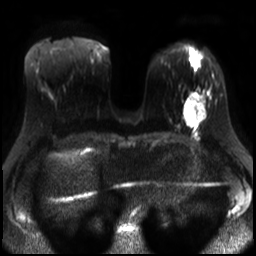
Breast MRI, one axial slice; slice 10 of 30 in the series (ordered by position); diffusion-weighted series; image 2 of 4 stored at this slice position (different b-values; order by instance number); 3 T; 256 × 256 image matrix. Female patient.
Annotated regions visible in this slice (outlined manually by an expert reader):
- tumour on diffusion-weighted imaging: bounding box (x1, y1, x2, y2) in pixels: (185, 95, 205, 126)